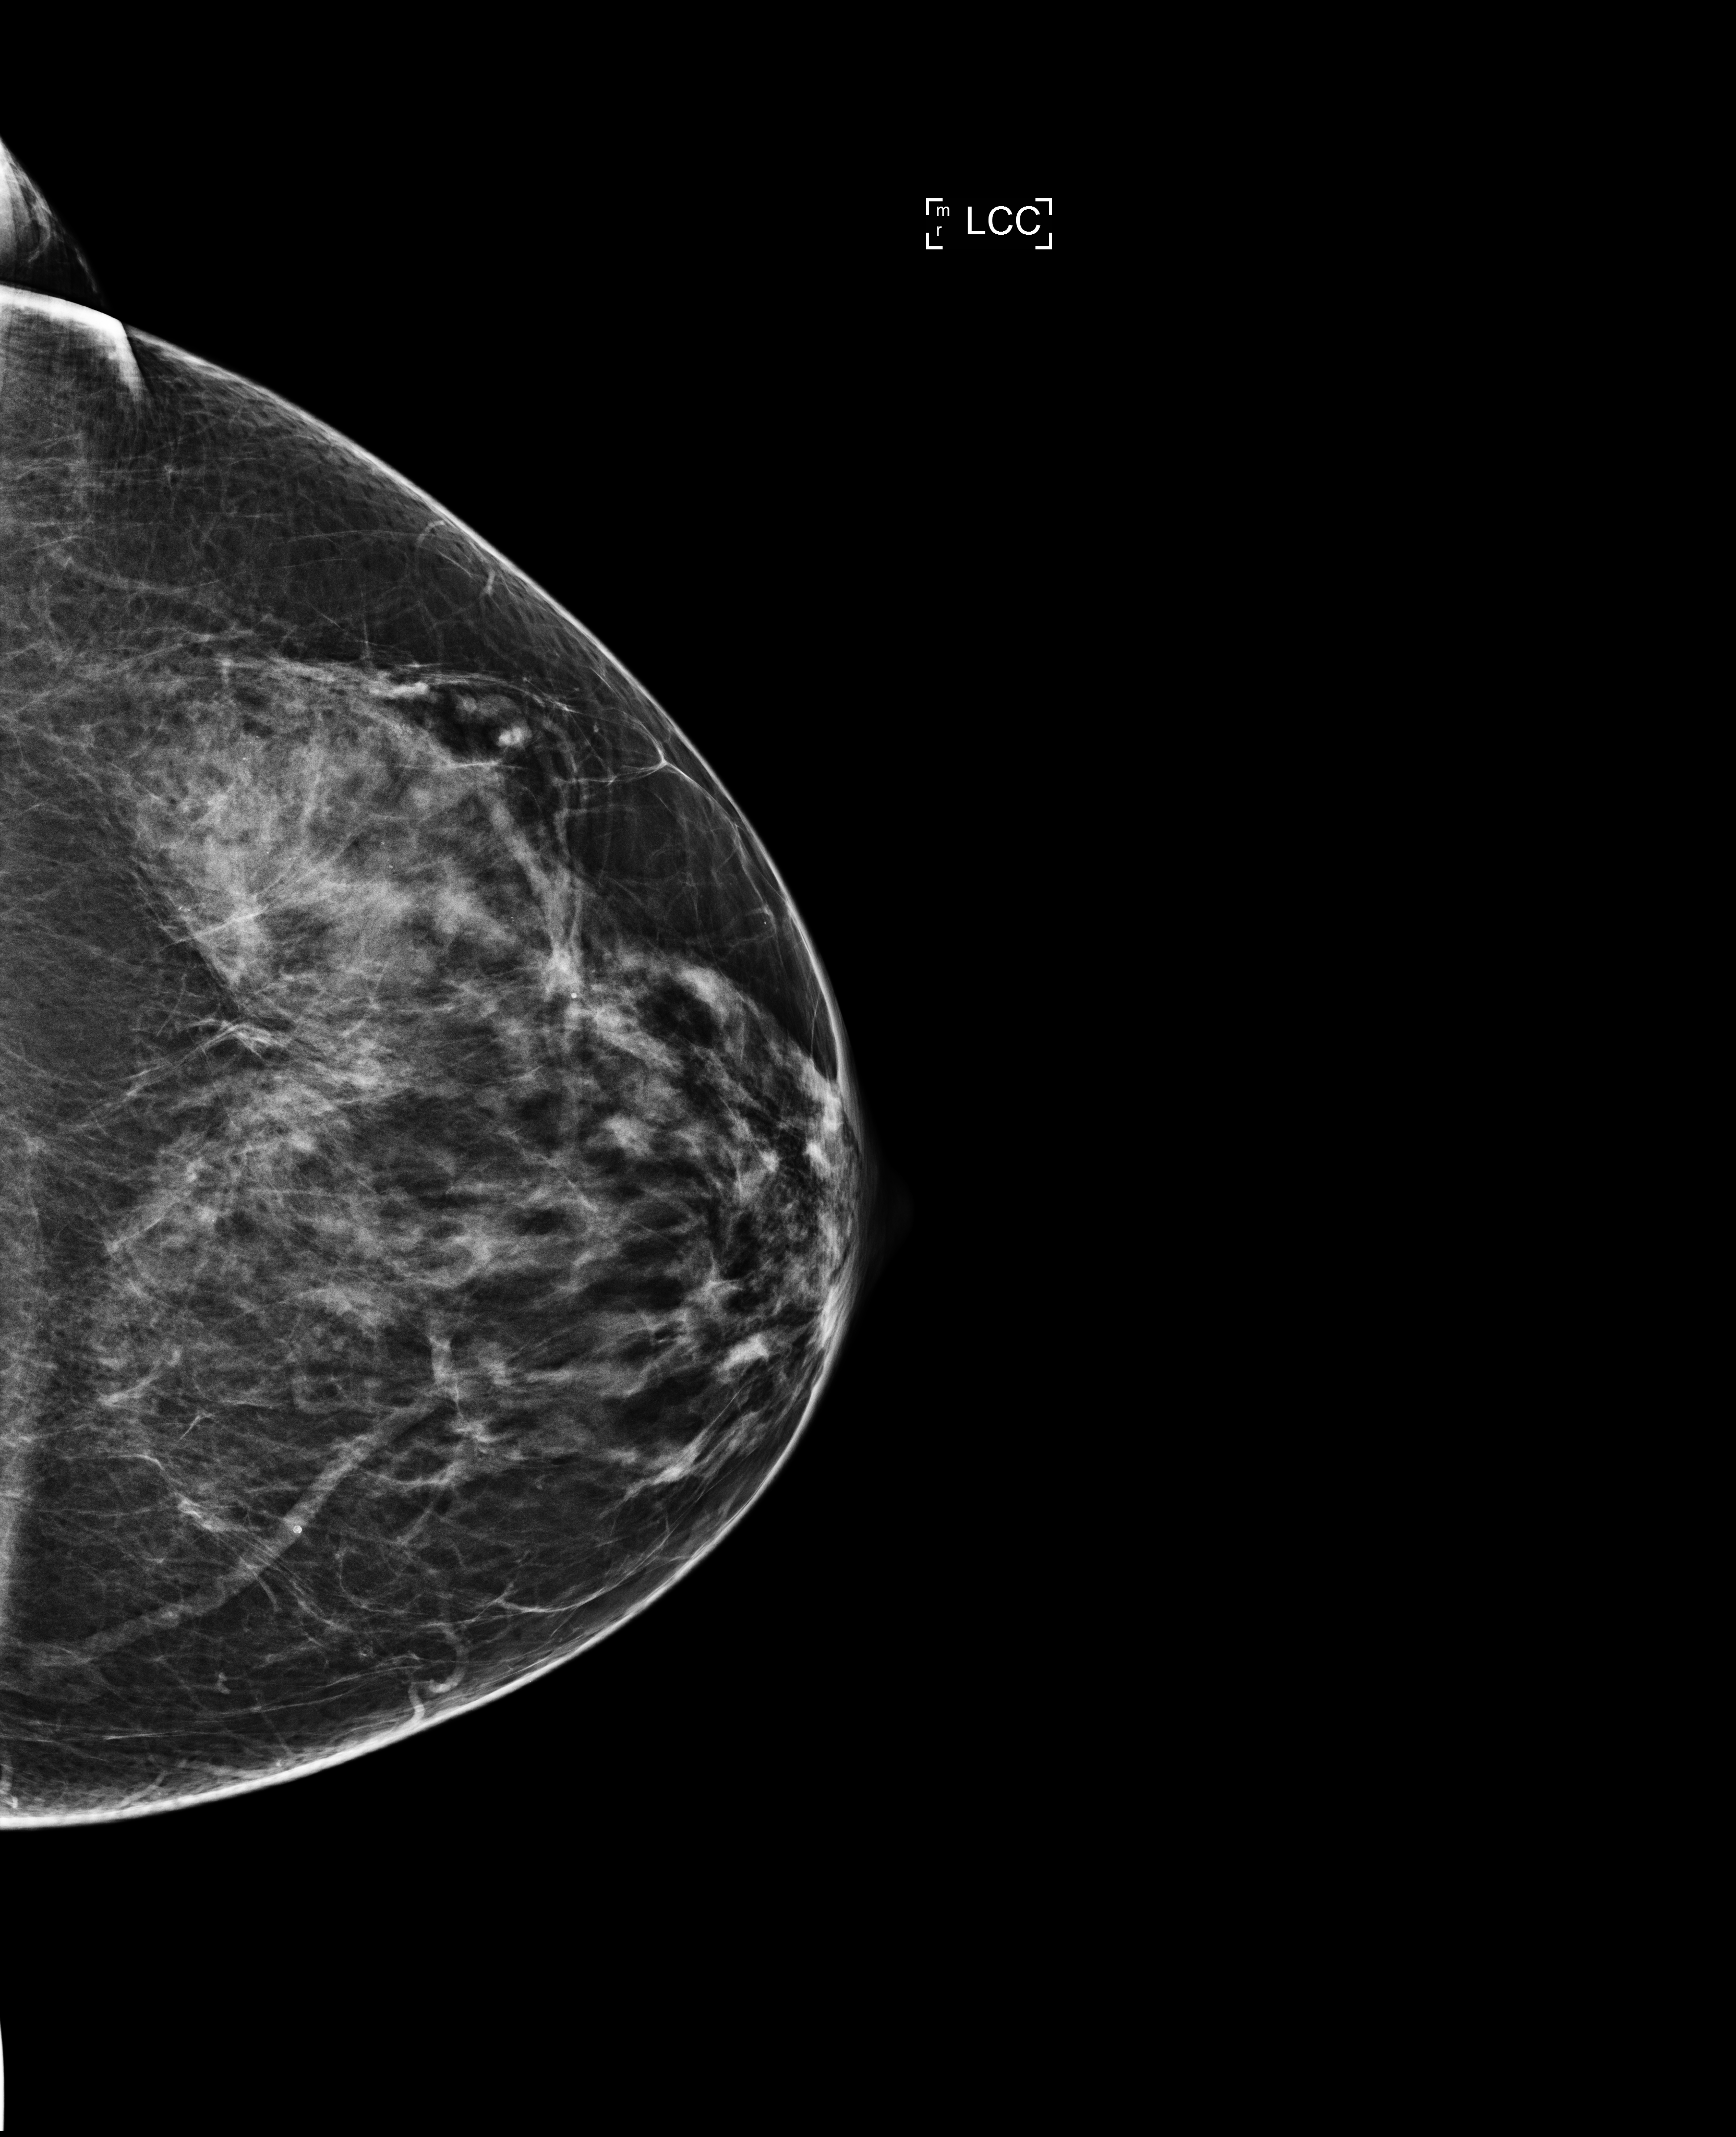
Screening examination. Patient aged 60 years (female).
Image type: full-field digital mammogram. Breast: left. Projection: cranio-caudal projection.